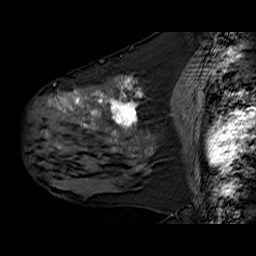
Breast MRI (dynamic contrast-enhanced), one sagittal slice. Slice 31 of 60 in the series (ordered by position). Dynamic contrast-enhanced series, time point 2 of 6 at this slice position (early post-contrast). 1.5 T. TE 6.3 ms, TR 32.9 ms. 256 × 256 image matrix, field of view 200 × 200 mm. Female patient. Case-level facts recorded for this patient, not image findings: setting: breast cancer imaged before/during neoadjuvant chemotherapy; receptor status: HER2-positive.
Structures marked on this image (semi-automatic segmentation, software-assisted and operator-edited):
- analysis volume of interest (the breast-tissue region the enhancement analysis was run in; not a lesion): bounding box <30,78,154,180> (left, top, right, bottom; pixels)
- tumour enhancement mask (voxels above the 100 % enhancement threshold inside the analysis volume of interest): <48,78,136,151>